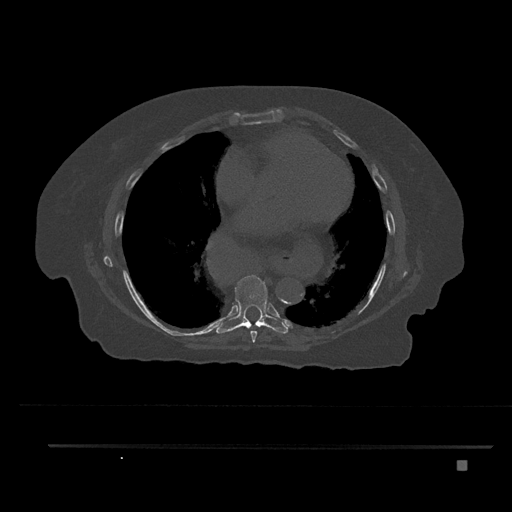
CT including the spine, one axial slice; position 454 of 797 along the scan axis; reconstruction kernel Br40s/3; 120 kVp; bone window (W 1800 / L 400 HU); 512 × 512 image matrix, field of view 437 × 437 mm. Patient: female, 76 years. Case-level facts recorded for this patient, not image findings: primary cancer: lung; vertebrae with lytic lesions (as recorded): T11, L3.
Outlined on this slice (semi-automatic segmentation, software-assisted and operator-edited):
- T7 vertebra: bounding box (x1, y1, x2, y2) in pixels: (250, 330, 257, 343)
- T8 vertebra: (216, 275, 288, 334)